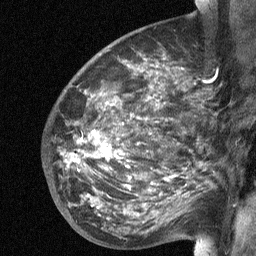
Breast MRI (dynamic contrast-enhanced), one sagittal slice; position 39 of 64 along the scan axis; dynamic contrast-enhanced study with each time point stored as its own series, time point 2 of 3 at this slice position (early post-contrast, ordered by acquisition time); 1.5 T; TE 4.8 ms, TR 27 ms; 2 mm slice thickness; 256 × 256 image matrix. Female patient, age 50 years. From the clinical record (not read from this slice): setting: breast cancer imaged before/during neoadjuvant chemotherapy; receptor status: HER2-positive.
Structures marked on this image (semi-automatic segmentation, software-assisted and operator-edited):
- analysis volume of interest (the breast-tissue region the enhancement analysis was run in; not a lesion): box from (x=62, y=91) to (x=204, y=226) px
- tumour enhancement mask (voxels above the 90 % enhancement threshold inside the analysis volume of interest): (x=73, y=147)–(x=110, y=160)